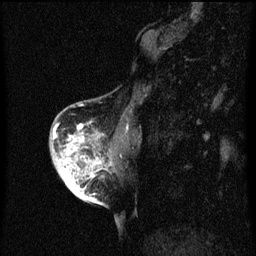
Breast MRI (dynamic contrast-enhanced), one sagittal slice. Position 20 of 60 along the scan axis. Dynamic contrast-enhanced series, image 2 of 3 at this slice position (ordered by acquisition). 1.5 T. TE 4.2 ms, TR 8 ms. 2 mm slice thickness. 256 × 256 image matrix, field of view 180 × 180 mm. Patient: female, 56 years.
Structures marked on this image (semi-automatically segmented with operator editing):
- analysis volume of interest (the breast-tissue region the enhancement analysis was run in; not a lesion): bounding box (x1, y1, x2, y2) in pixels: (54, 122, 115, 199)
- tumour enhancement mask (voxels above the 70 % enhancement threshold inside the analysis volume of interest): (54, 126, 102, 199)